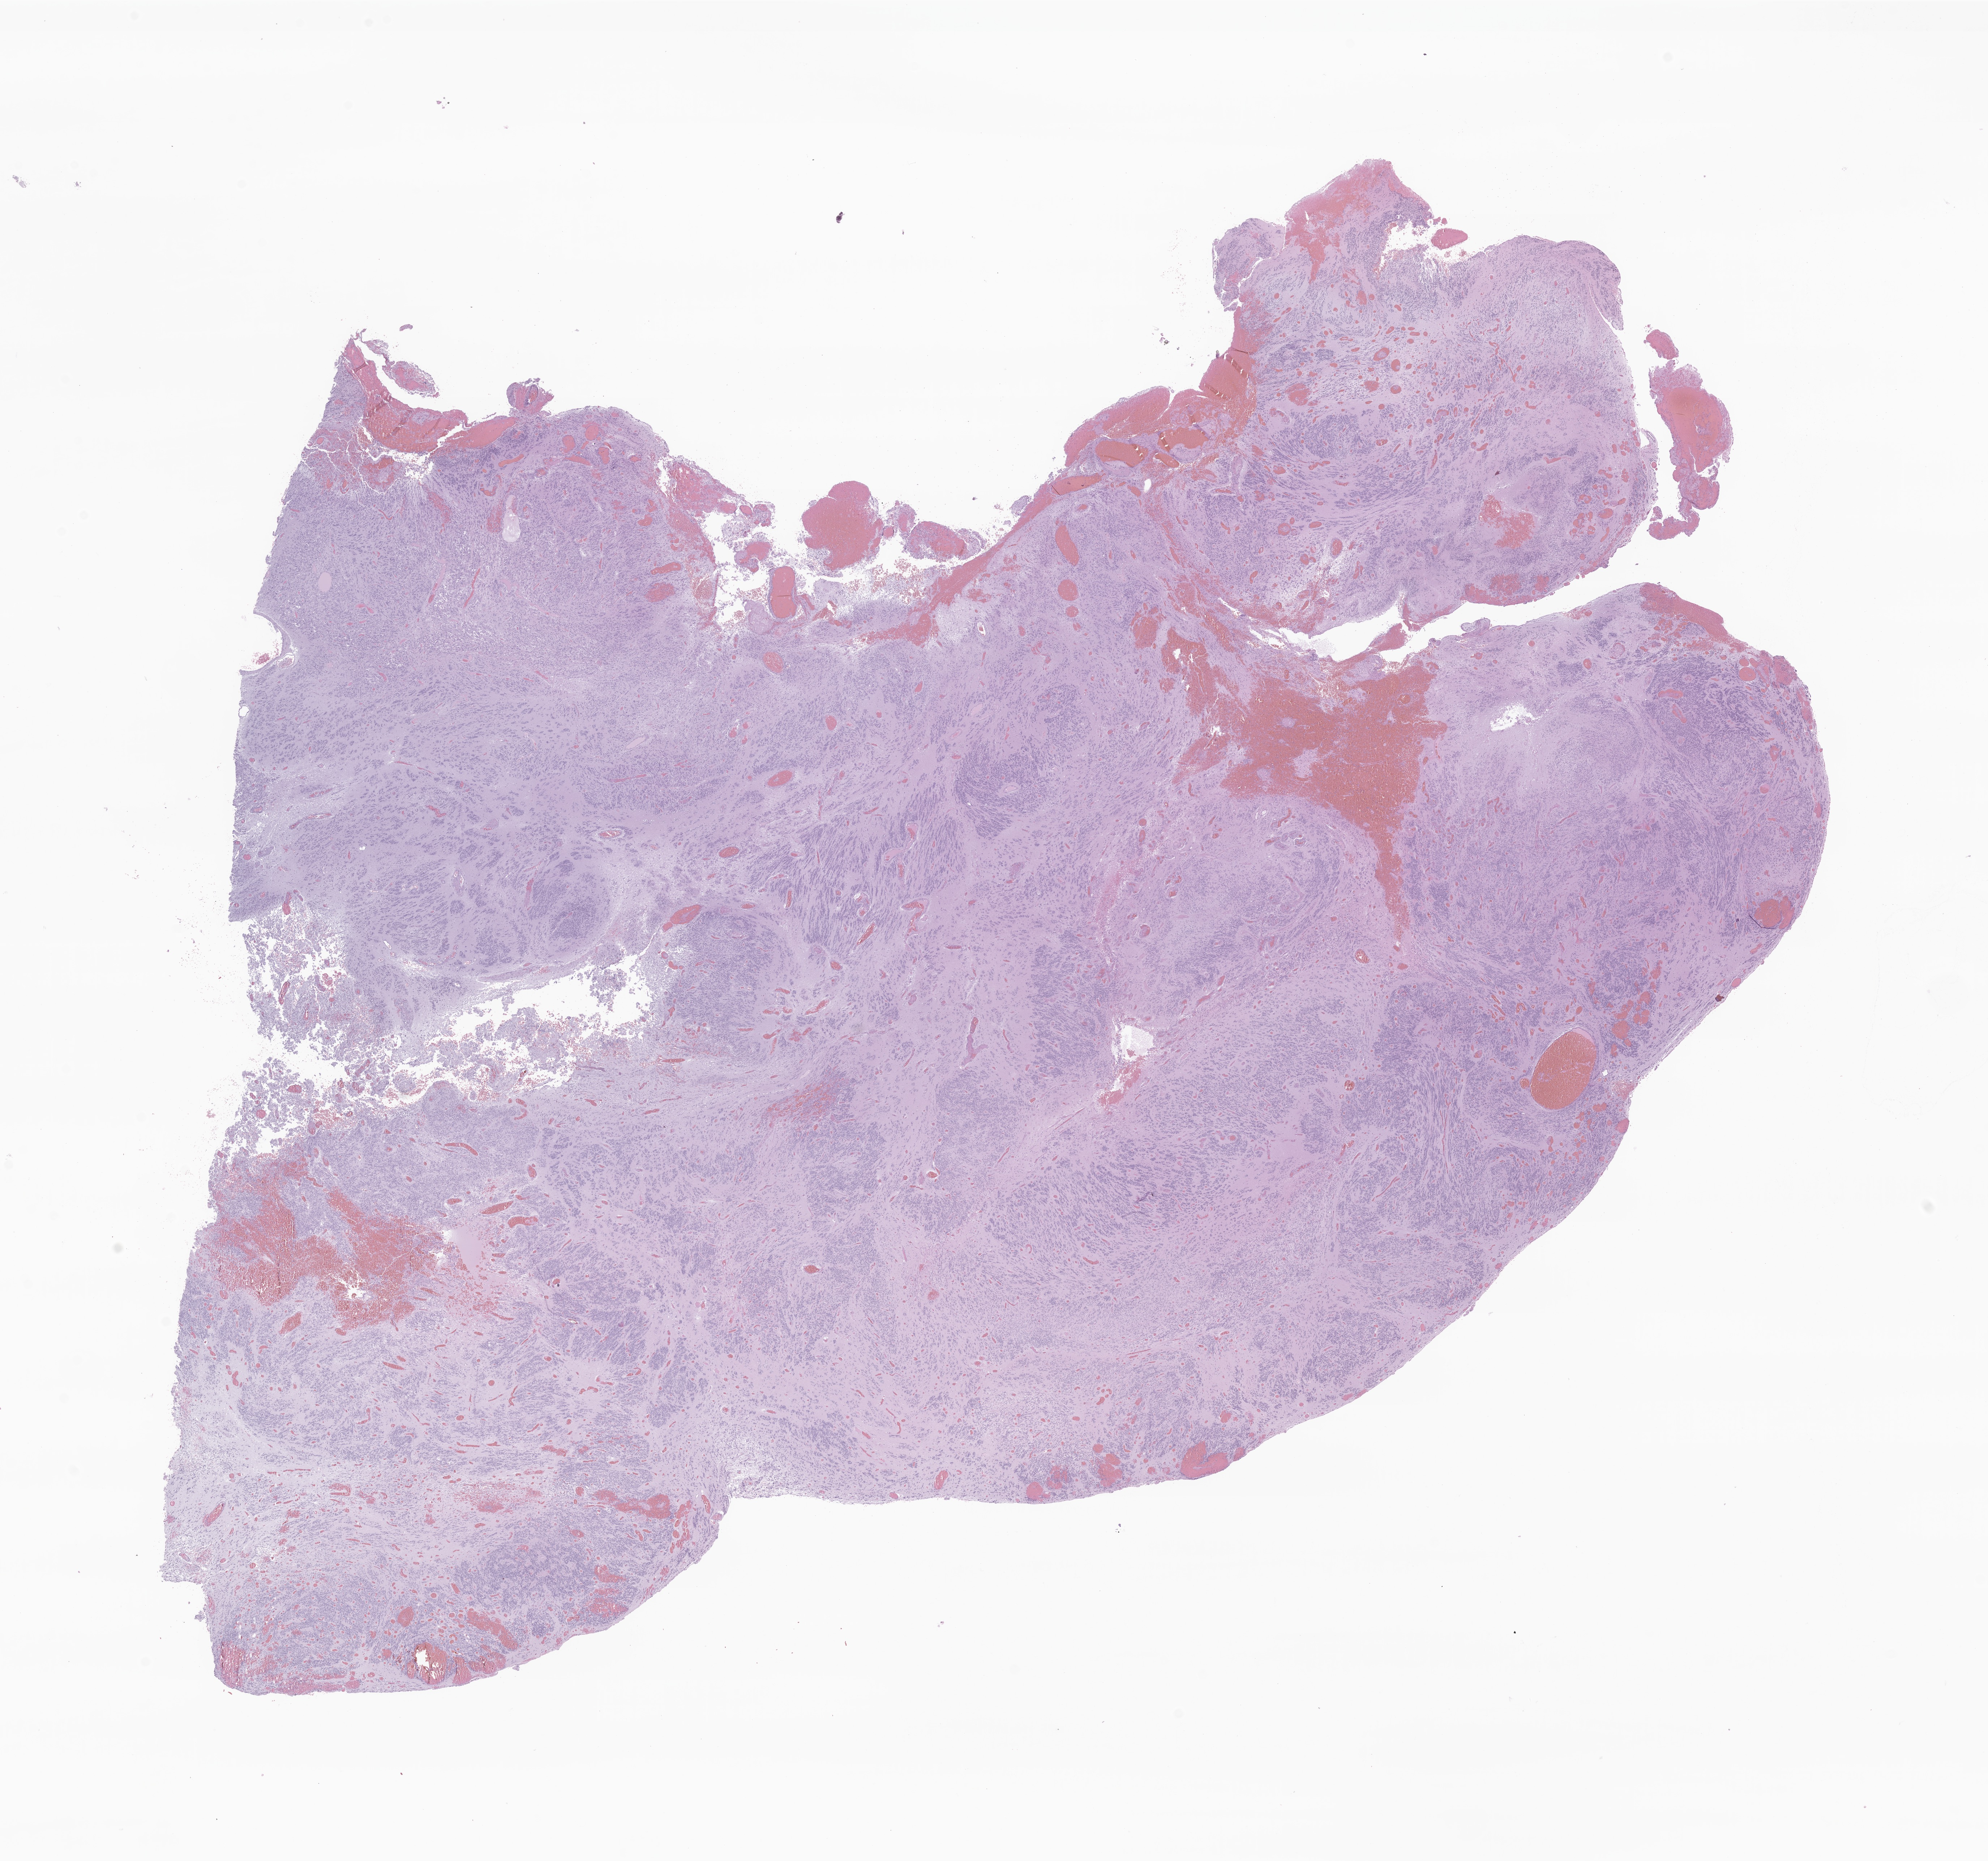
Whole-slide image, H&E stain of tumor tissue from the brain — a low-resolution overview of the entire scanned area, about 23.2 x 21.7 mm; formalin-fixed paraffin-embedded section. Patient: female, age 185 months (15 years 5 months).
Diagnosis (ICD-O-3 morphology term): Neoplasm, uncertain whether benign or malignant.